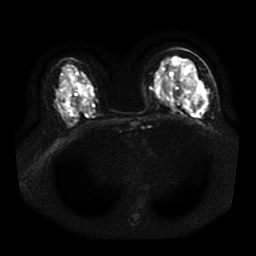
Breast MRI, one axial slice; position 22 of 41 along the scan axis; diffusion-weighted series; image 2 of 4 stored at this slice position (different b-values; order by instance number); 1.5 T; 256 × 256 image matrix, field of view 330 × 330 mm. Female patient.
Structures marked on this image (expert manual segmentation):
- tumour on diffusion-weighted imaging: bounding box [x1, y1, x2, y2] px = [182, 78, 206, 107]